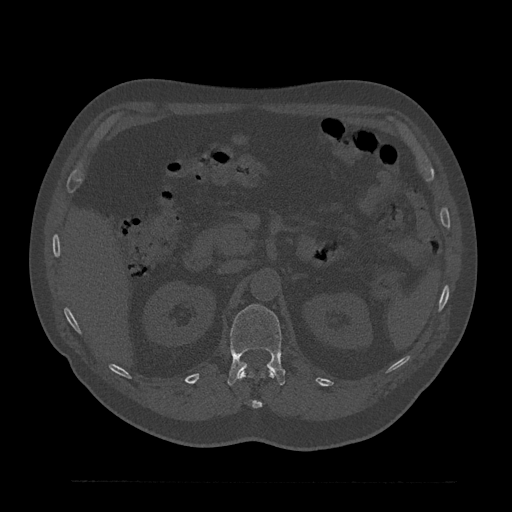
CT including the spine, one axial slice; position 187 of 797 along the scan axis; bone window (W 1800 / L 400 HU); 512 × 512 image matrix, field of view 430 × 430 mm. Male patient, age 61 years. Case-level facts recorded for this patient, not image findings: primary cancer: prostate.
Structures marked on this image (semi-automatically segmented with operator editing):
- L1 vertebra: bounding box <228,304,285,386> (left, top, right, bottom; pixels)
- T12 vertebra: <238,371,275,409>